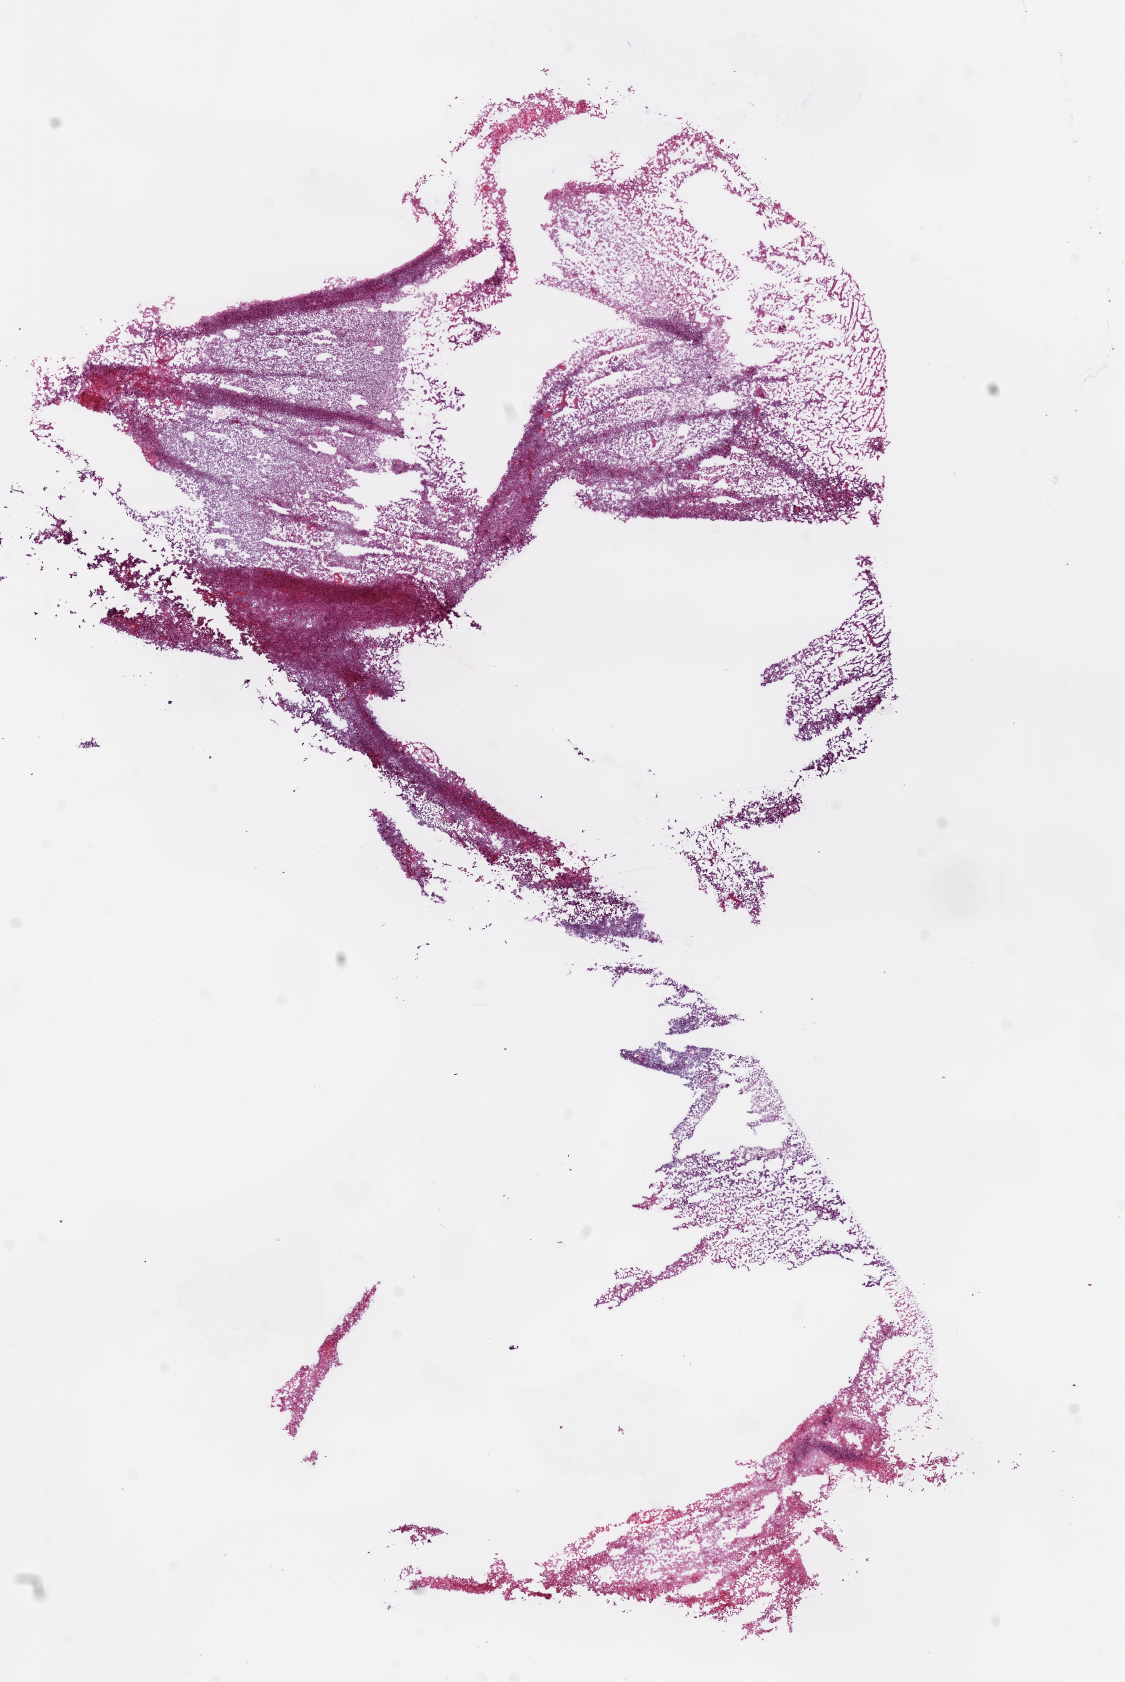
Digitized H&E-stained tissue section (whole slide) — a low-resolution overview of the entire scanned area, about 9.0 x 13.5 mm (from a 20x scan); frozen section from the bottom of the tissue portion; brain, primary tumour sample. Female, age 44 years at initial diagnosis. Slide review estimates, as recorded: tumour cells 70%, tumour nuclei 85%, normal cells 0%, stromal cells 0%, necrosis 30%.
Pathologic diagnosis: Glioblastoma.